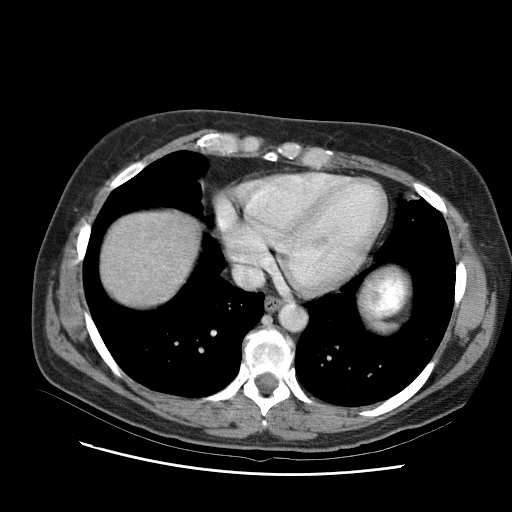
Contrast-enhanced abdominal CT (liver protocol), one axial slice; position 88 of 95 along the scan axis; 120 kVp; one of 2 acquisitions stored at this slice position; soft-tissue window (W 400 / L 40 HU); 2.5 mm slice thickness; 512 × 512 image matrix. From the clinical record (not read from this slice): diagnosis: hepatocellular carcinoma (patient treated with transarterial chemoembolisation; whether this scan precedes or follows treatment is not stated here); TNM stage (as recorded): Stage-I.
Outlined on this slice (semi-automatically segmented with operator editing):
- liver parenchyma outside the tumour (the mass and vessels are separate outlines, so this box may not span the whole liver): bounding box <120,218,170,272> (left, top, right, bottom; pixels)